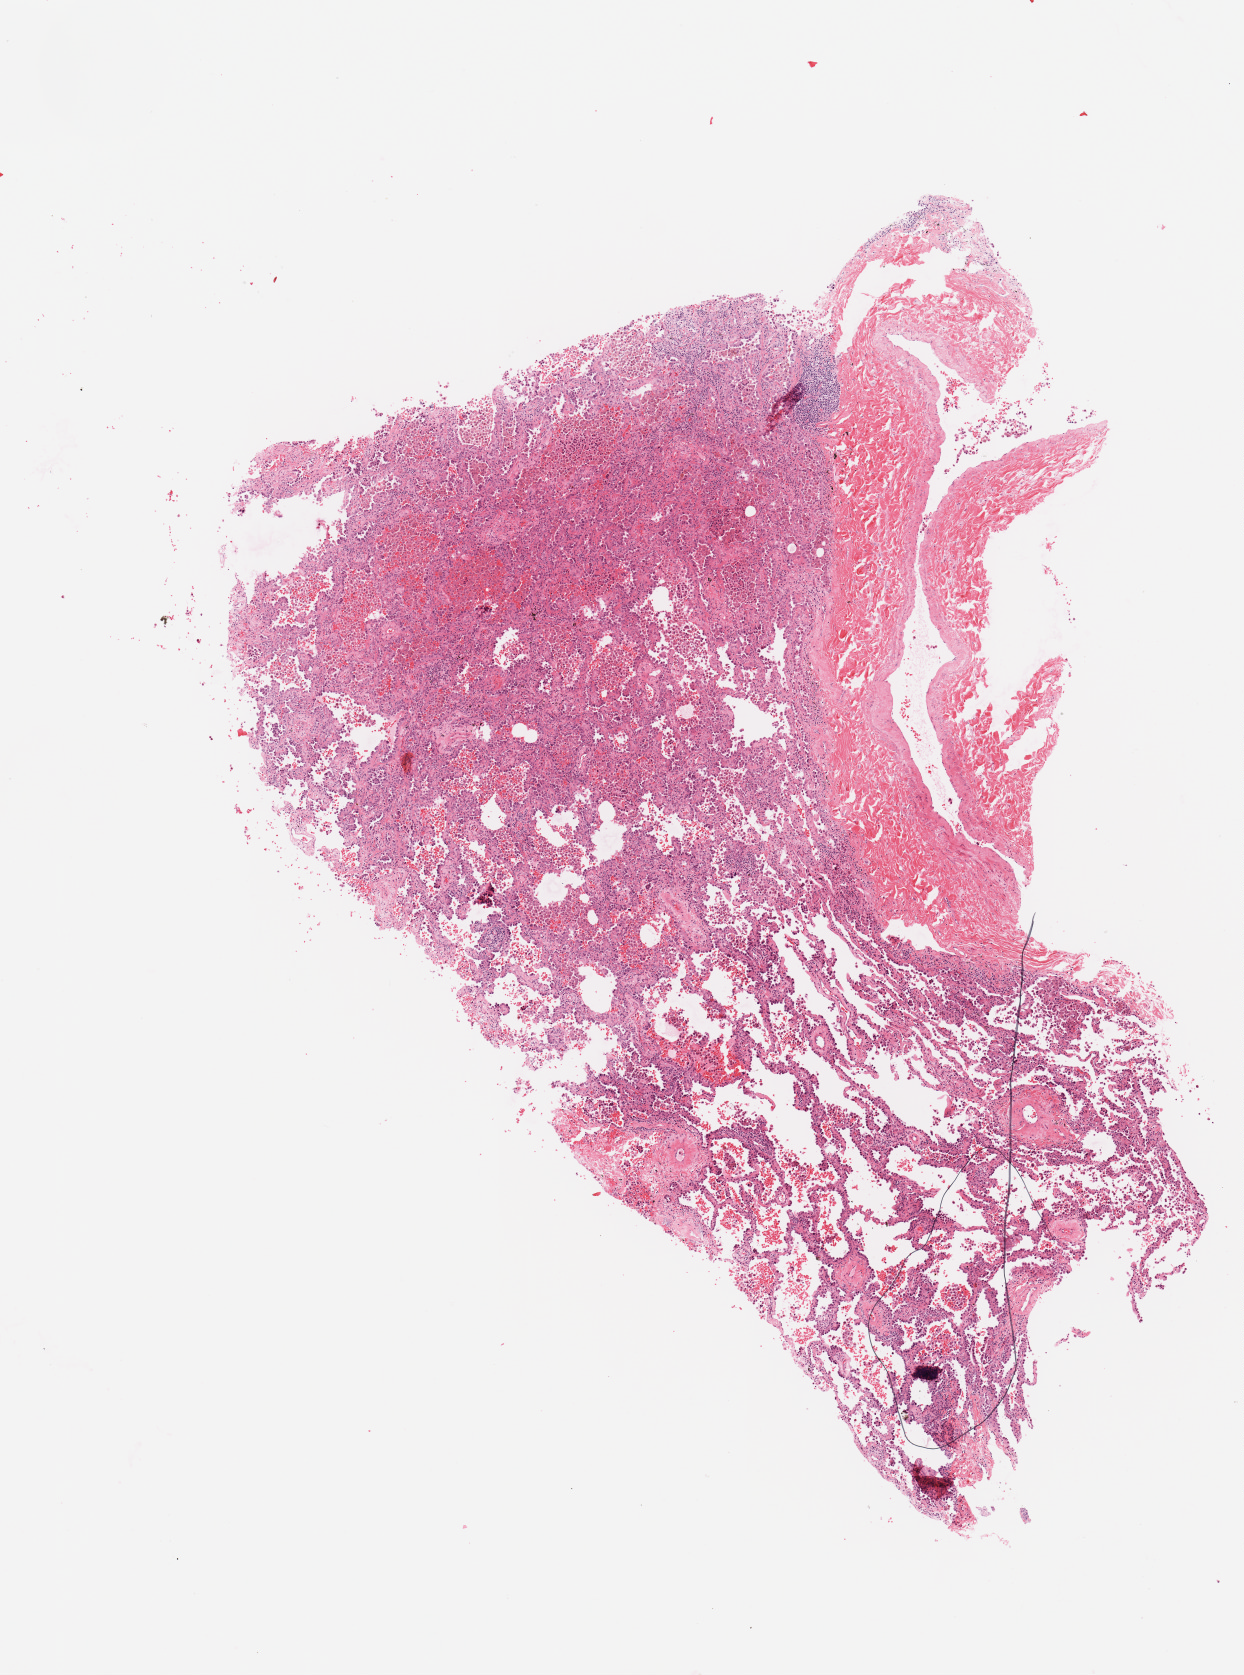
H&E-stained whole-slide image — shown as a low-resolution overview of the whole scanned area (about 4.9 x 6.6 mm). Lung, tumour tissue. Patient: female, age 70 years. Histologic grade: G2 (moderately differentiated).
Histologic diagnosis: Adenocarcinoma, NOS. AJCC pathologic stage: IIIA.